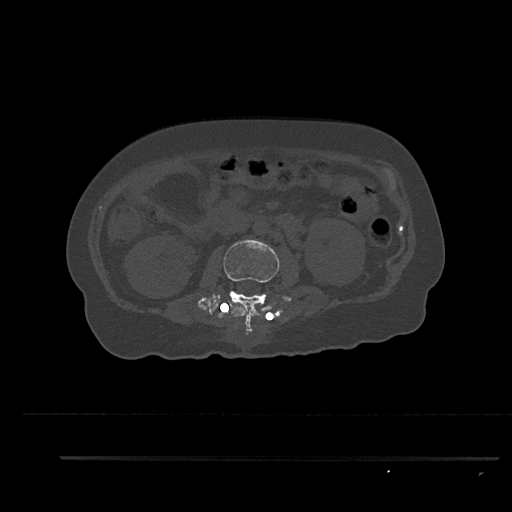
CT including the spine, one axial slice; slice 143 of 797 in the series (ordered by position); 120 kVp; bone window (W 1800 / L 400 HU); 512 × 512 image matrix. Female patient, age 44 years. From the clinical record (not read from this slice): primary cancer: renal.
Structures marked on this image (semi-automatic segmentation, software-assisted and operator-edited):
- L2 vertebra: box from (x=198, y=239) to (x=280, y=335) px